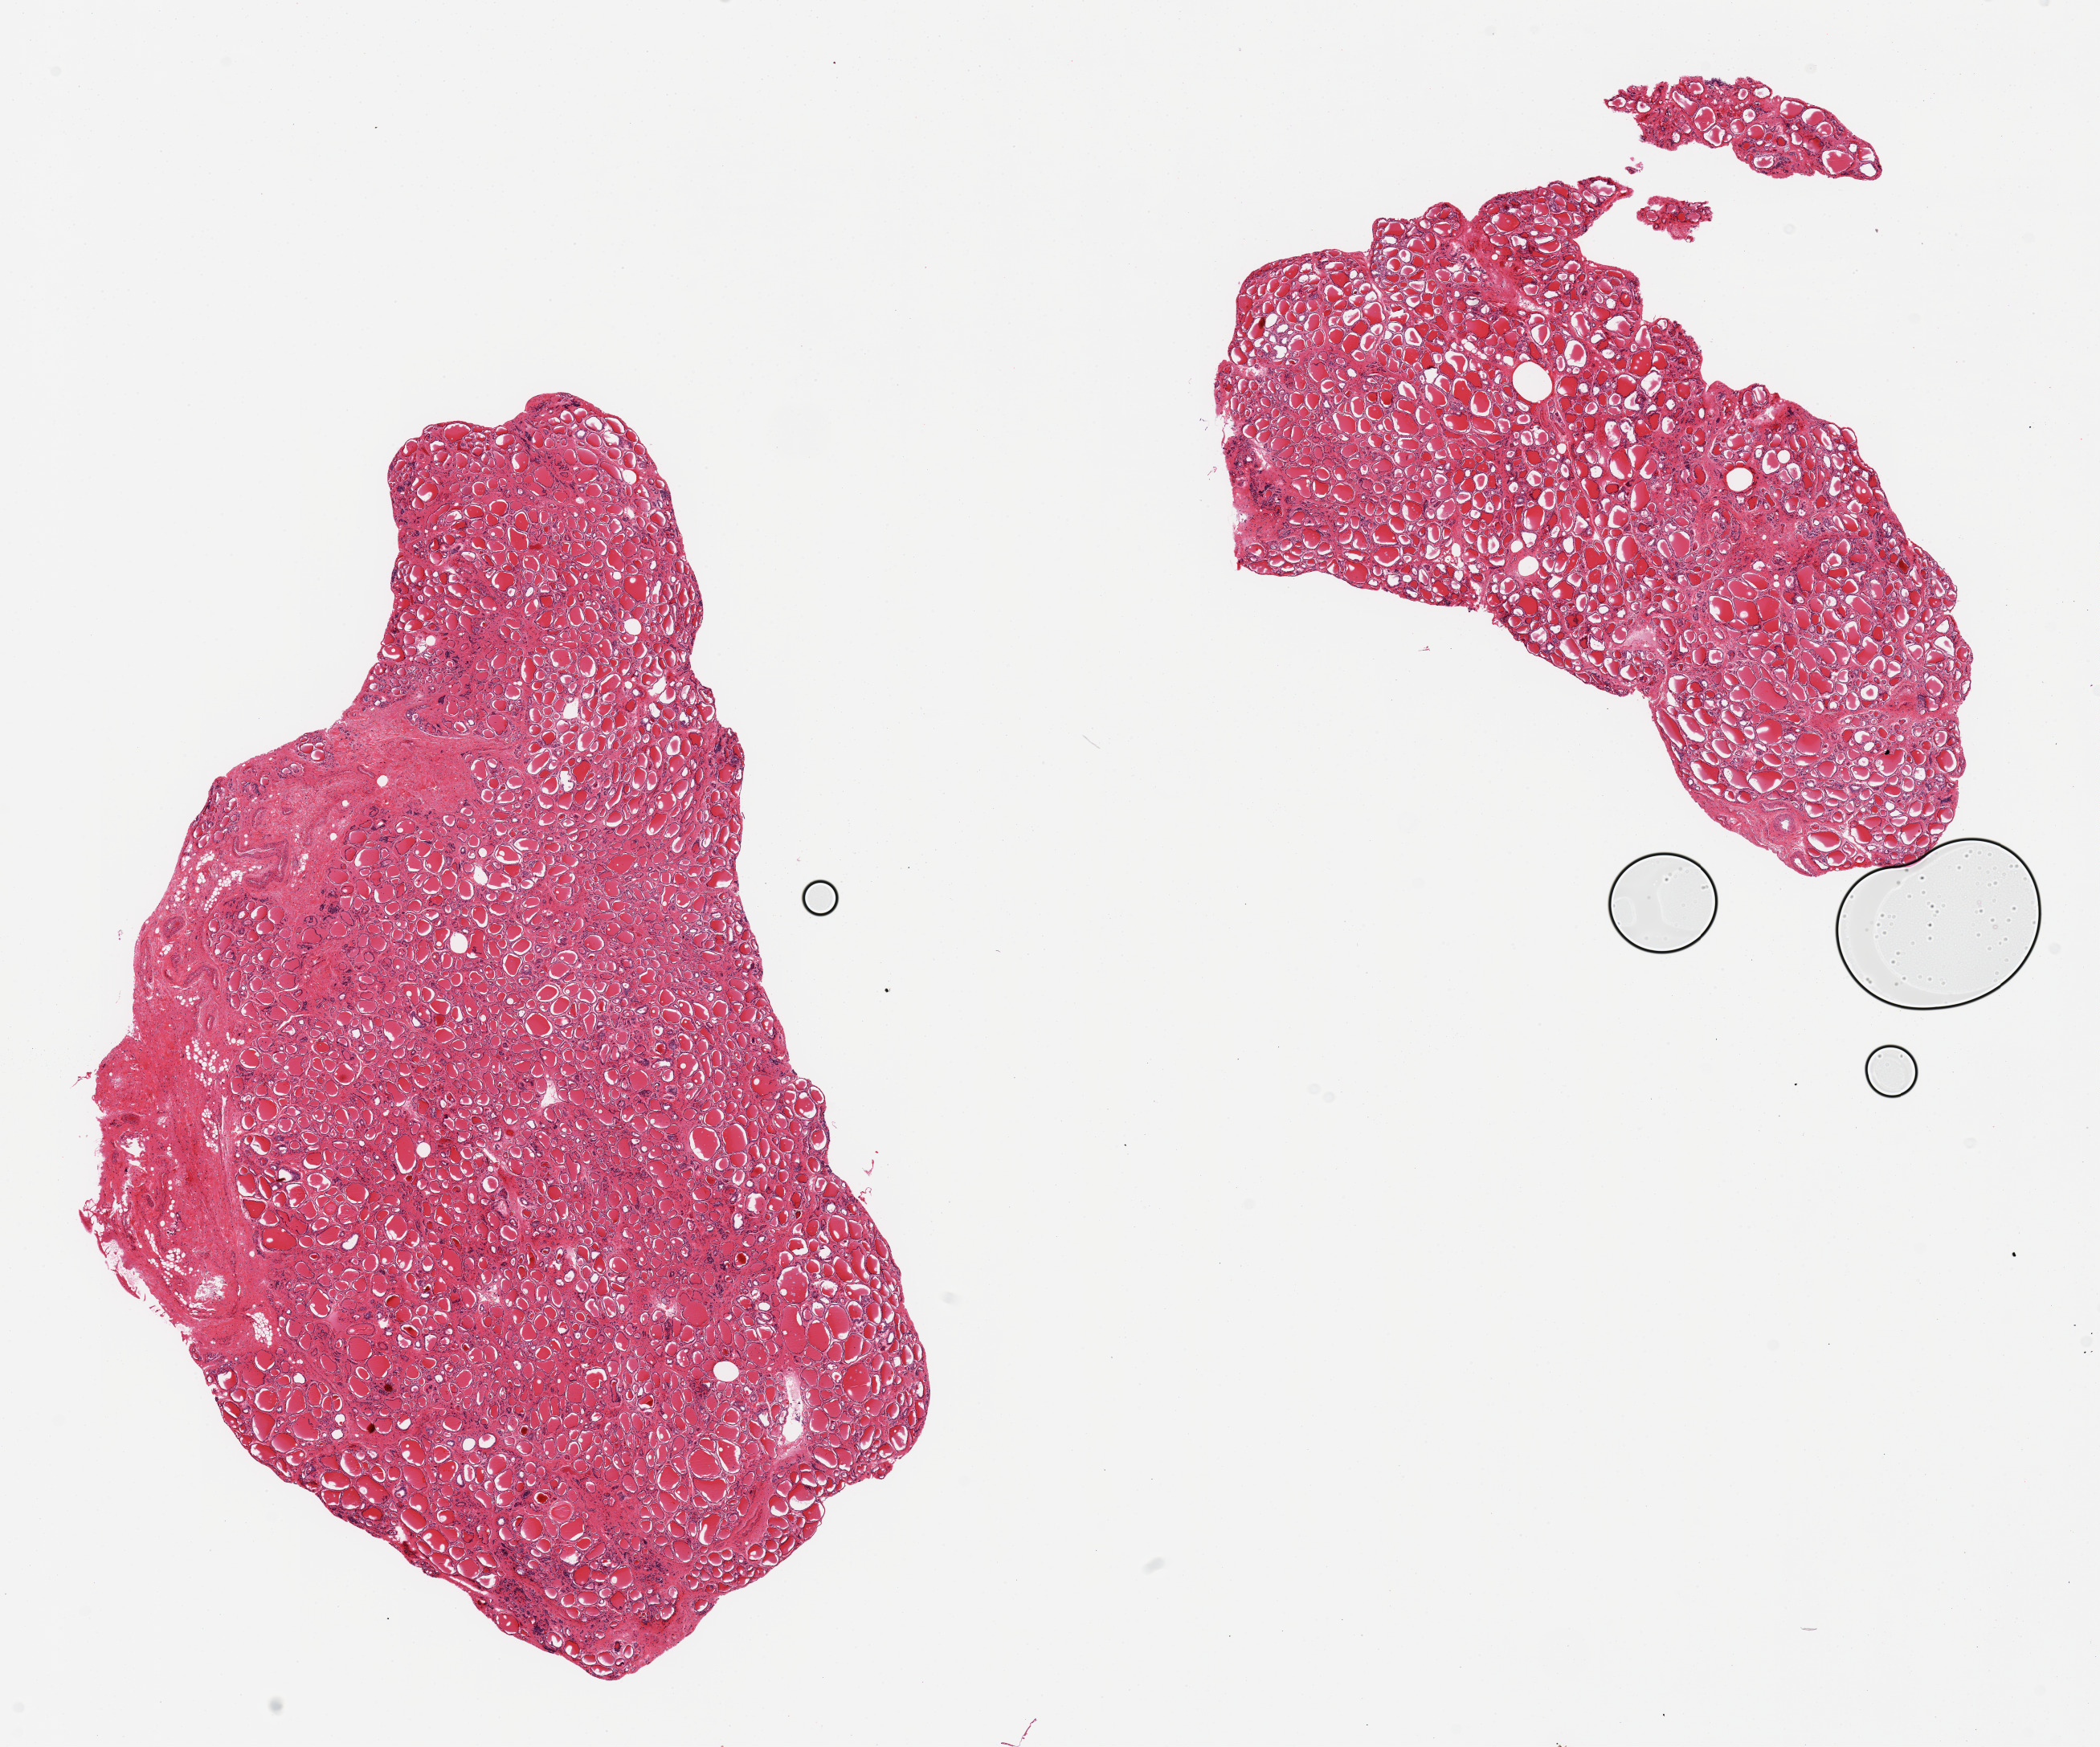
Whole-slide image, H&E stain, shown as a low-resolution overview of the whole scanned area (about 20.7 x 17.2 mm). PAXgene-fixed paraffin-embedded (PFPE) section. Sampled site (target tissue): thyroid. Tissue donor sample.
Review note (as recorded): 2 pieces, regressive changes.